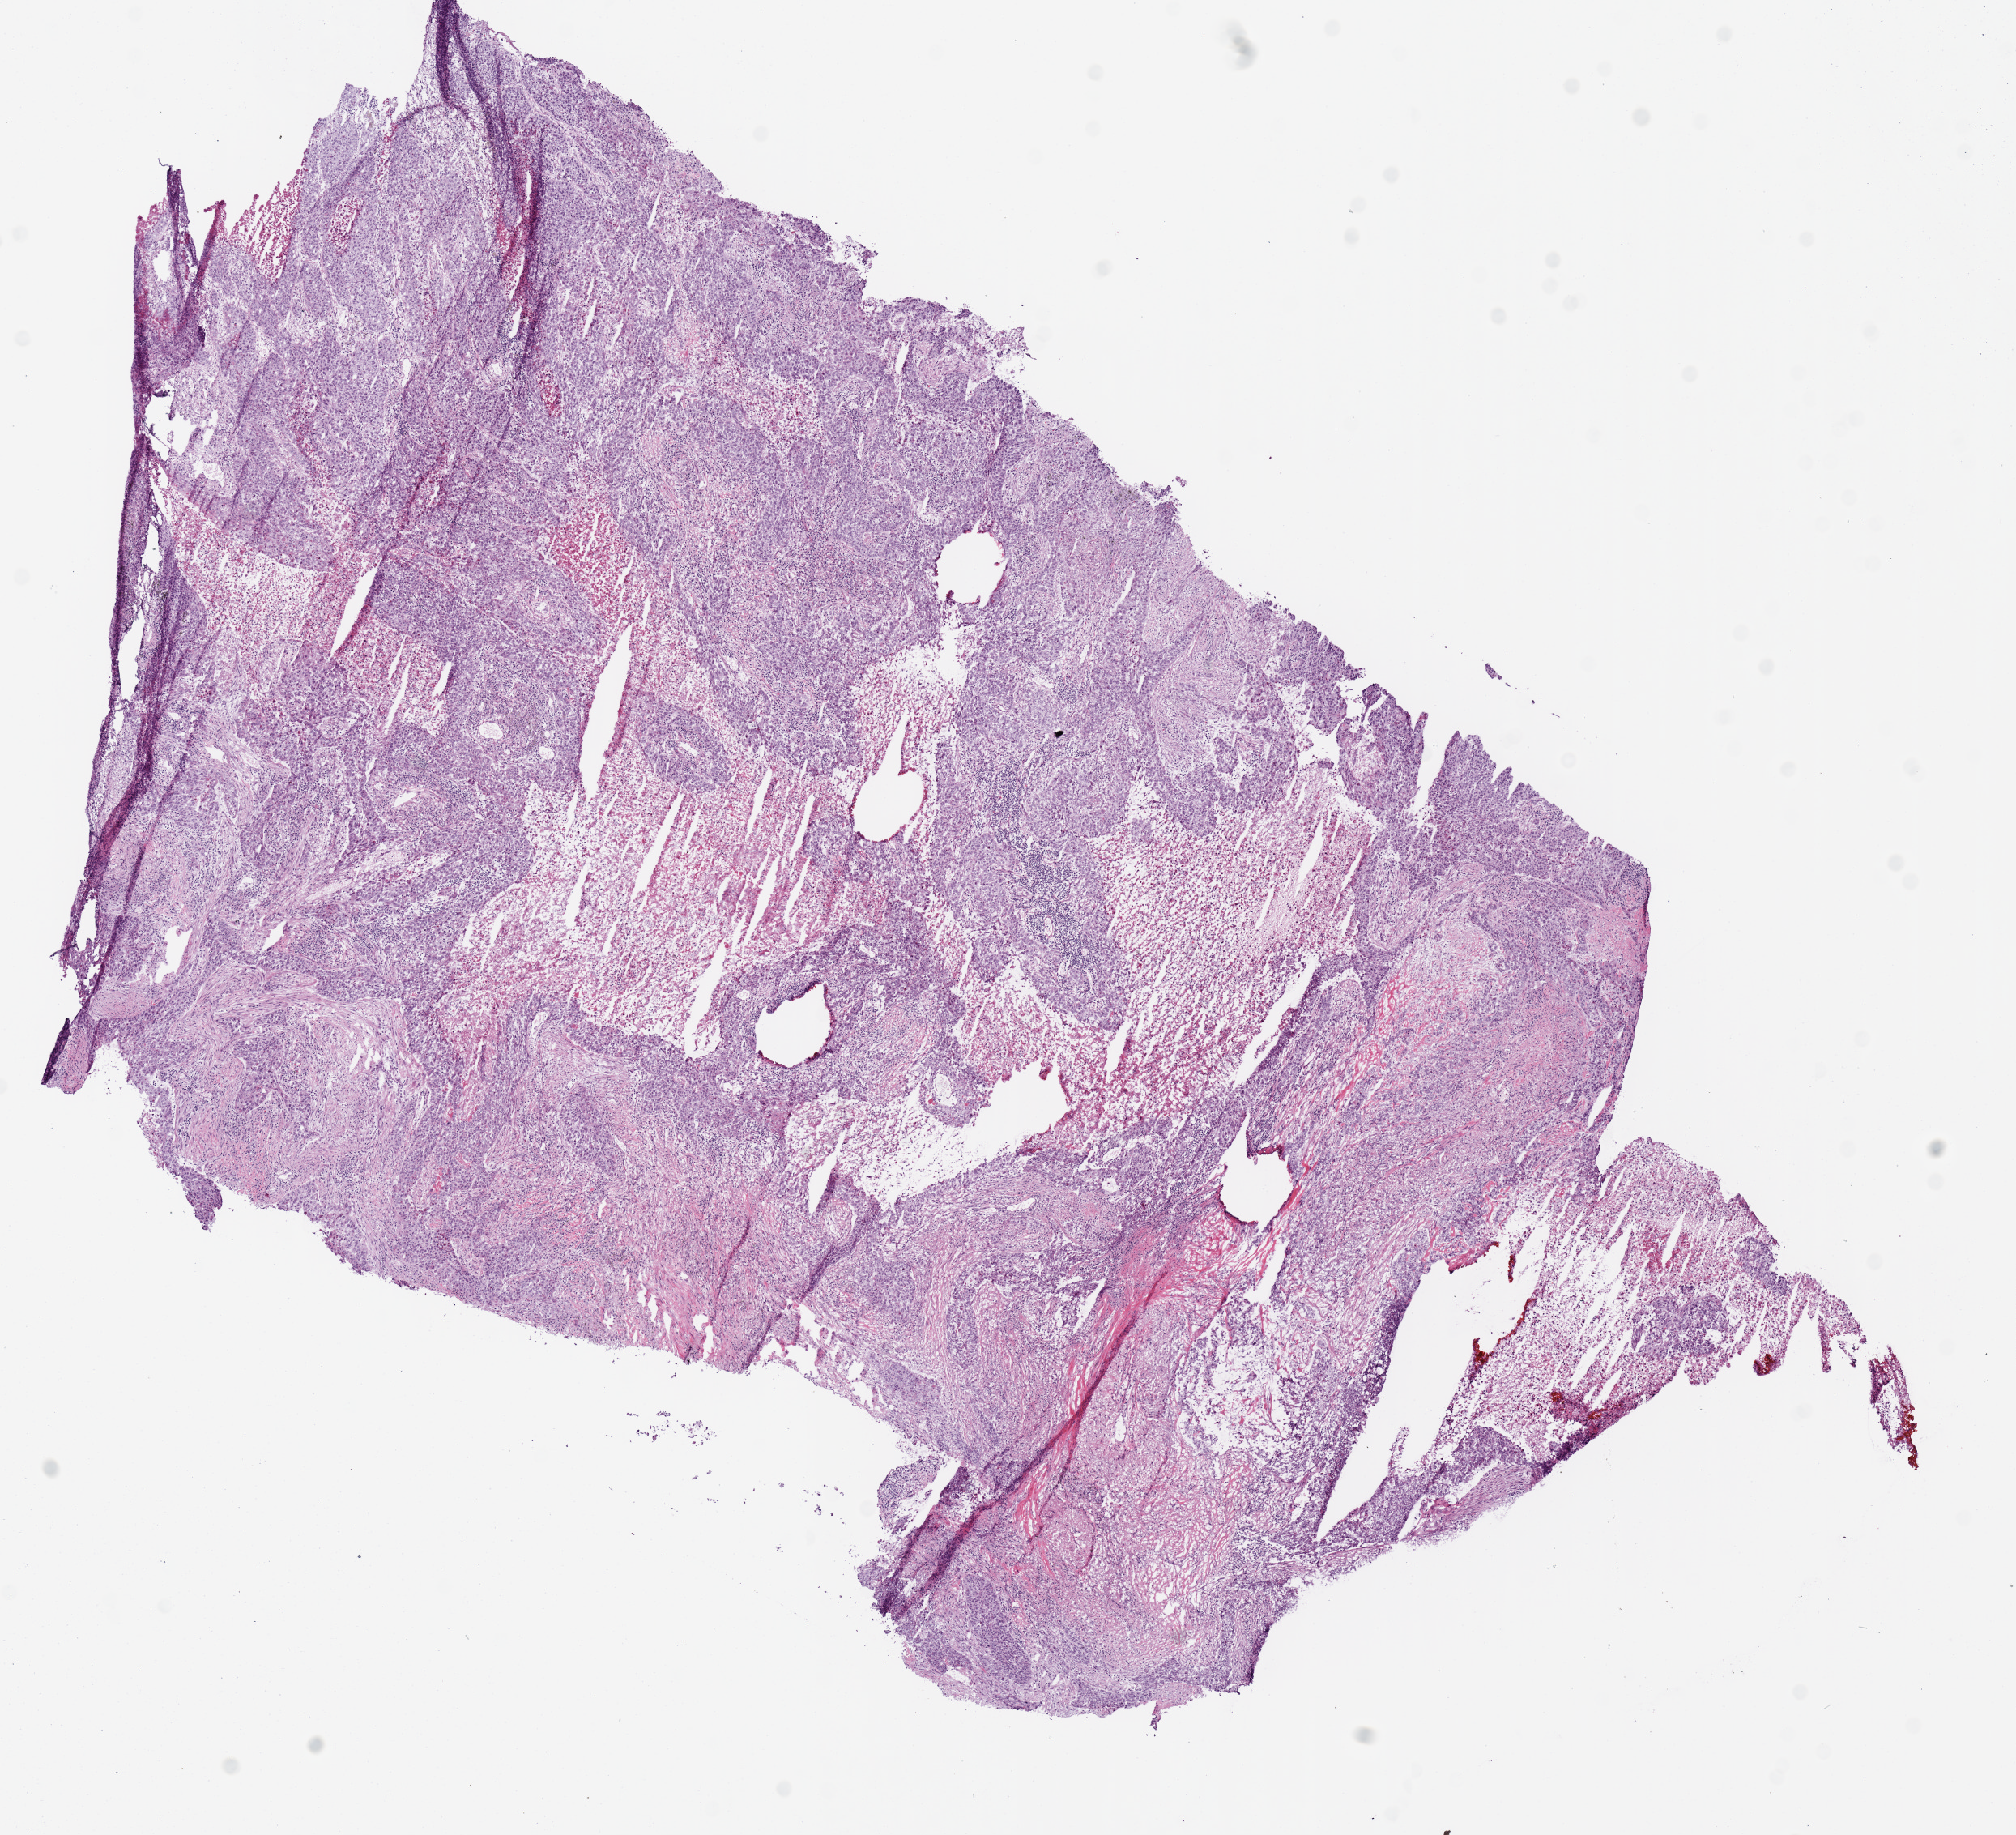
Digitized Hematoxylin and eosin (H&E) stained tissue section (whole slide) — a low-resolution overview of the entire scanned area, about 9.8 x 9.0 mm. Frozen section from the top of the tissue portion. Sample: primary tumour, lung. Patient: male, age at initial diagnosis 78 years. Slide review estimates, as recorded: tumour cells 75%, tumour nuclei 70%, normal cells 0%, stromal cells 10%, necrosis 15%.
* diagnosis: Squamous cell carcinoma, NOS (upper lobe, lung)
* TNM: T2a N0 M0
* AJCC pathologic stage: IB (7th edition)